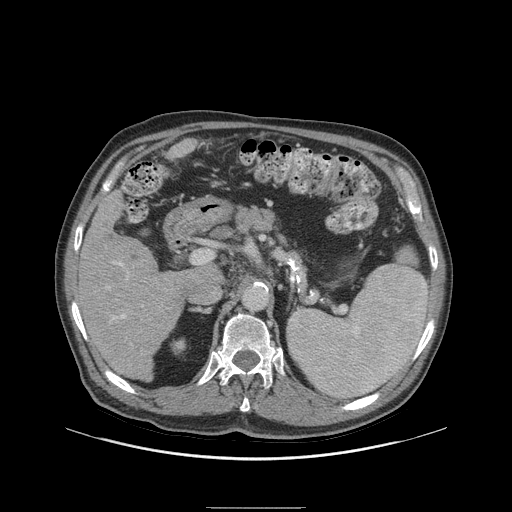
Contrast-enhanced abdominal CT (liver protocol), one axial slice; position 51 of 105 along the scan axis; reconstruction kernel STANDARD; 140 kVp; soft-tissue window (W 400 / L 40 HU); 2.5 mm slice thickness; 512 × 512 image matrix. From the clinical record (not read from this slice): diagnosis: hepatocellular carcinoma (patient treated with transarterial chemoembolisation; whether this scan precedes or follows treatment is not stated here); TNM stage (as recorded): Stage-I; Child-Pugh class: A; tumour size: 5.1 cm.
Outlined on this slice (semi-automatically segmented with operator editing):
- liver parenchyma outside the tumour (the mass and vessels are separate outlines, so this box may not span the whole liver): bounding box (x1, y1, x2, y2) in pixels: (76, 192, 194, 380)
- liver vessels: (107, 262, 126, 320)